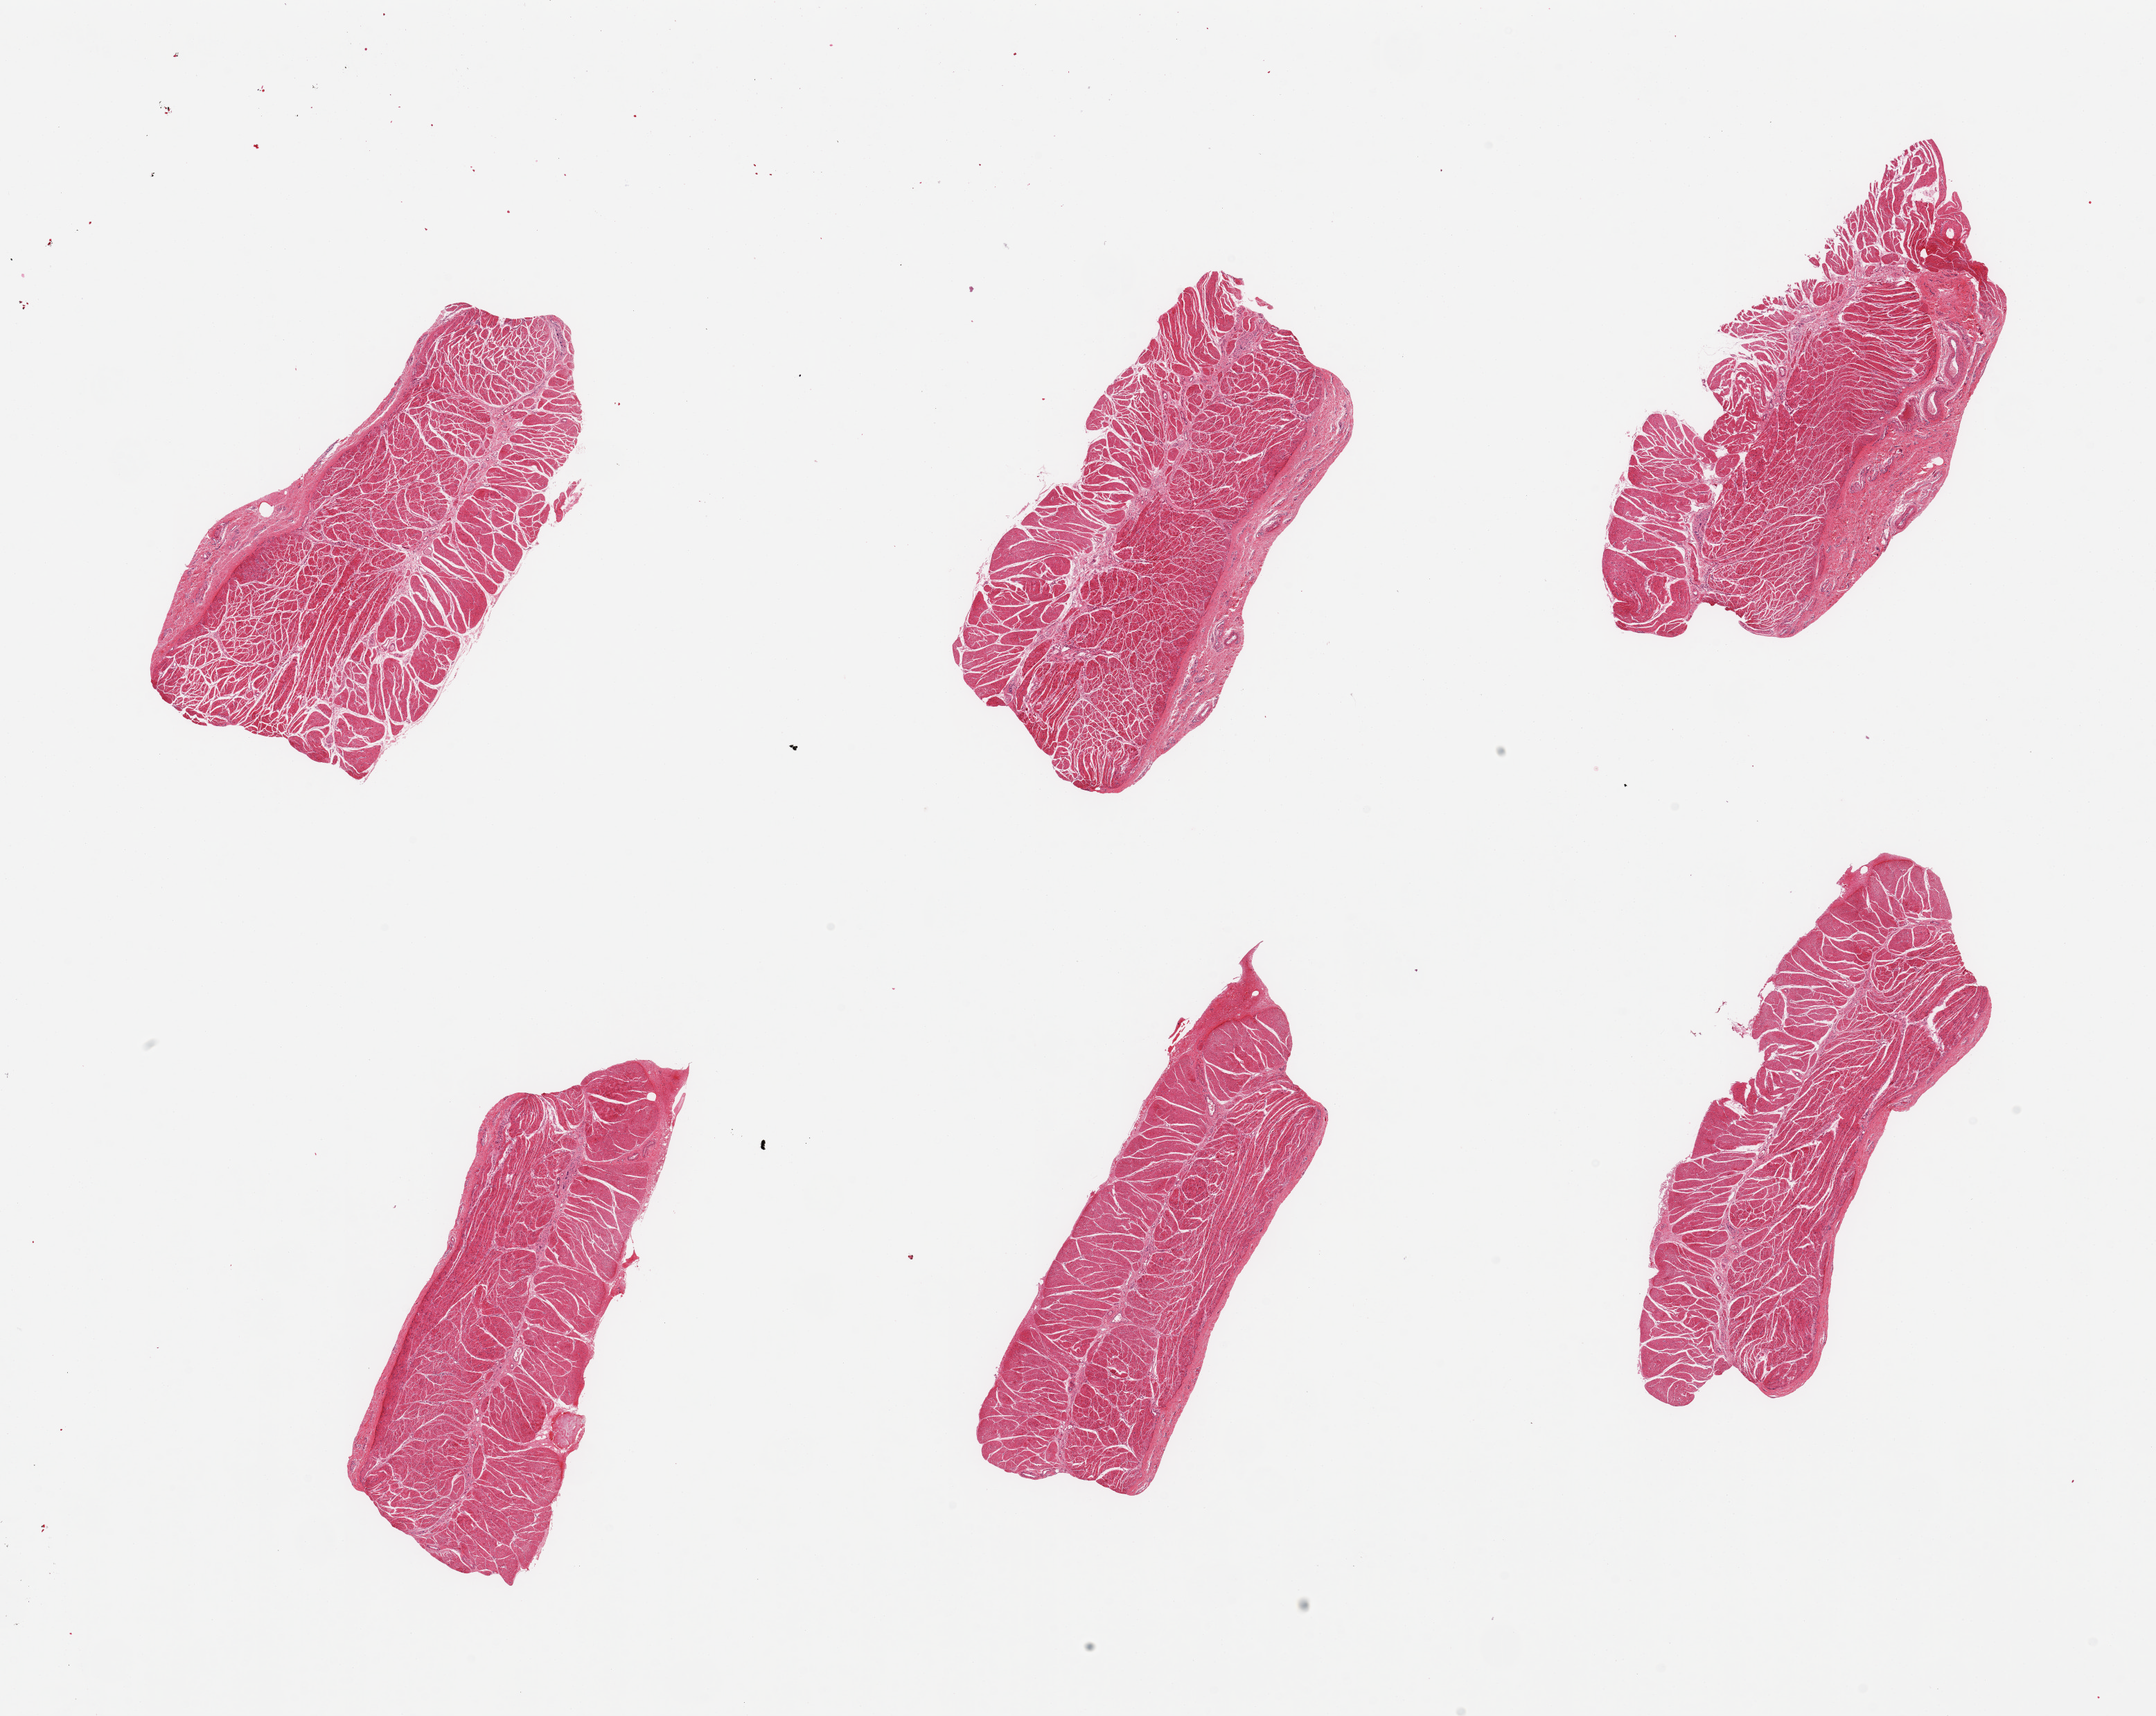
Haematoxylin and eosin whole-slide image — whole scanned area (about 24.6 x 19.6 mm) shown as a low-resolution overview. PAXgene-fixed paraffin-embedded (PFPE) section. Section of esophageal muscle (target tissue). Tissue donor sample. Male donor.
• pathologist's review note for this sample: 6 pieces, confirmed target muscularis